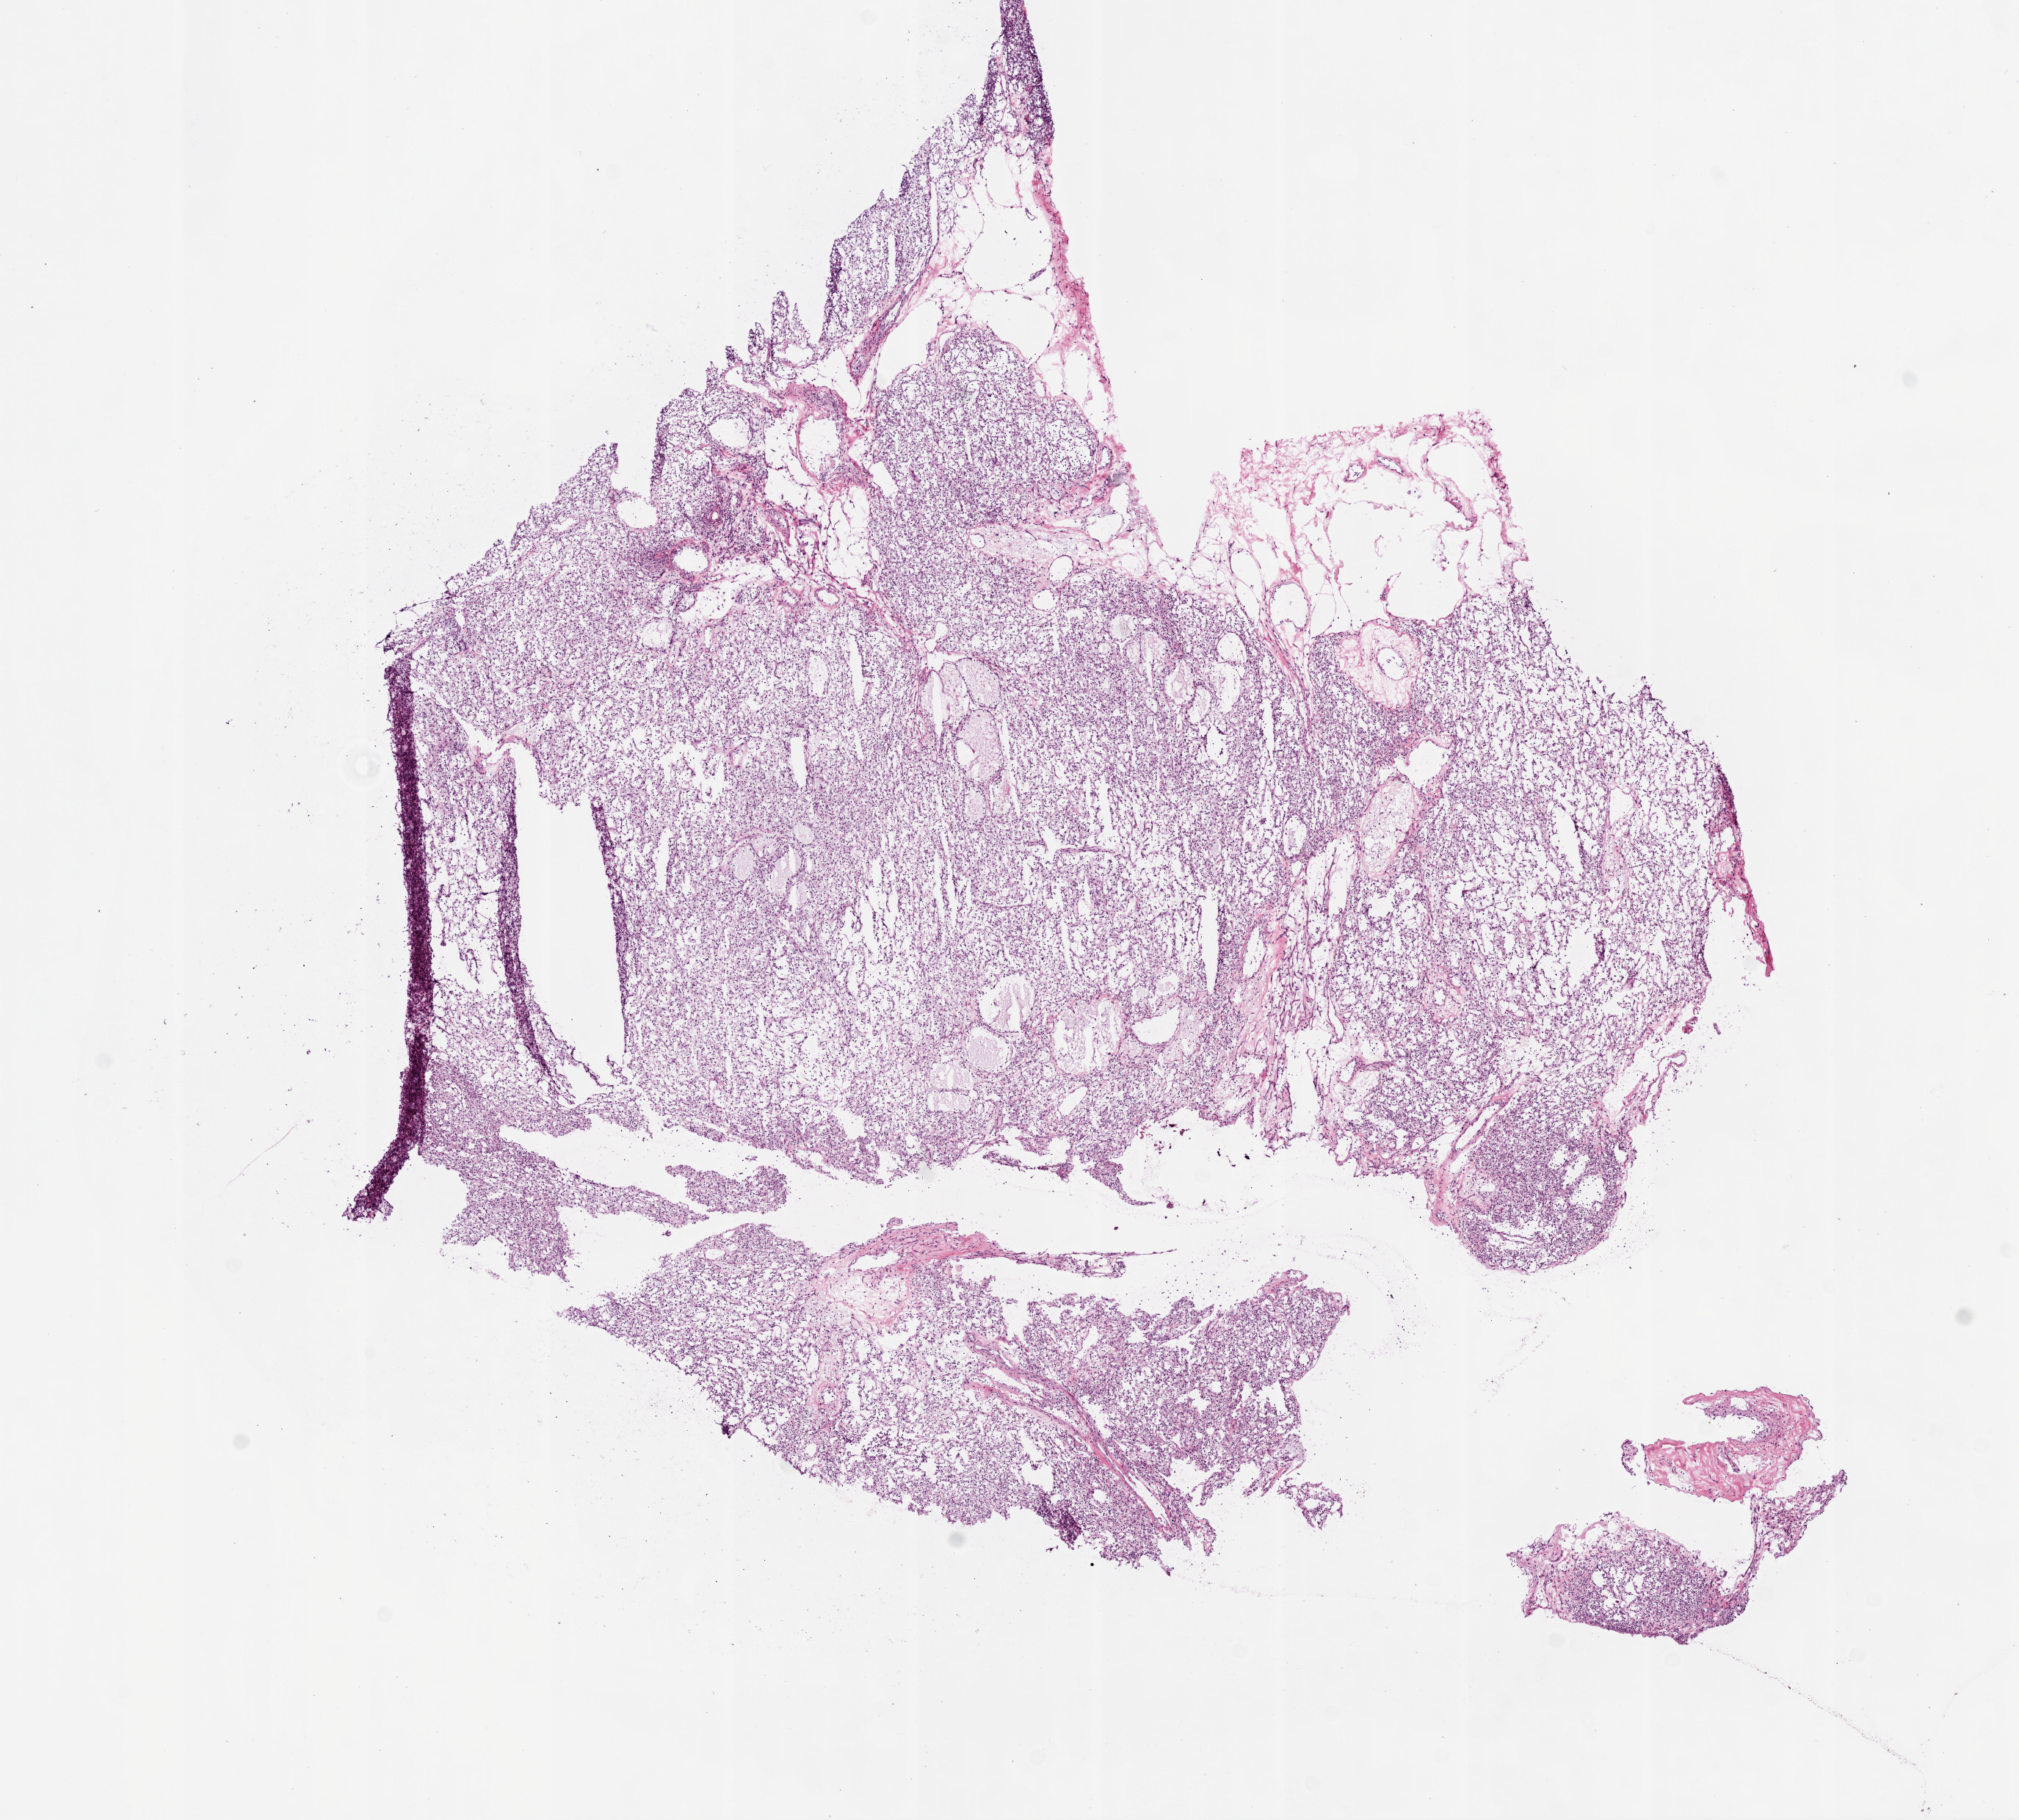
Digitized H&E tissue section (whole slide) — shown as a low-resolution overview of the whole scanned area (about 11.0 x 9.9 mm, from a 20x scan), frozen section, kidney, primary tumour sample. Female patient; age at initial diagnosis 53 years. Composition of this section per pathologist review: tumour cells 90%, tumour nuclei 80%.
Histologic diagnosis: Clear cell adenocarcinoma, NOS.